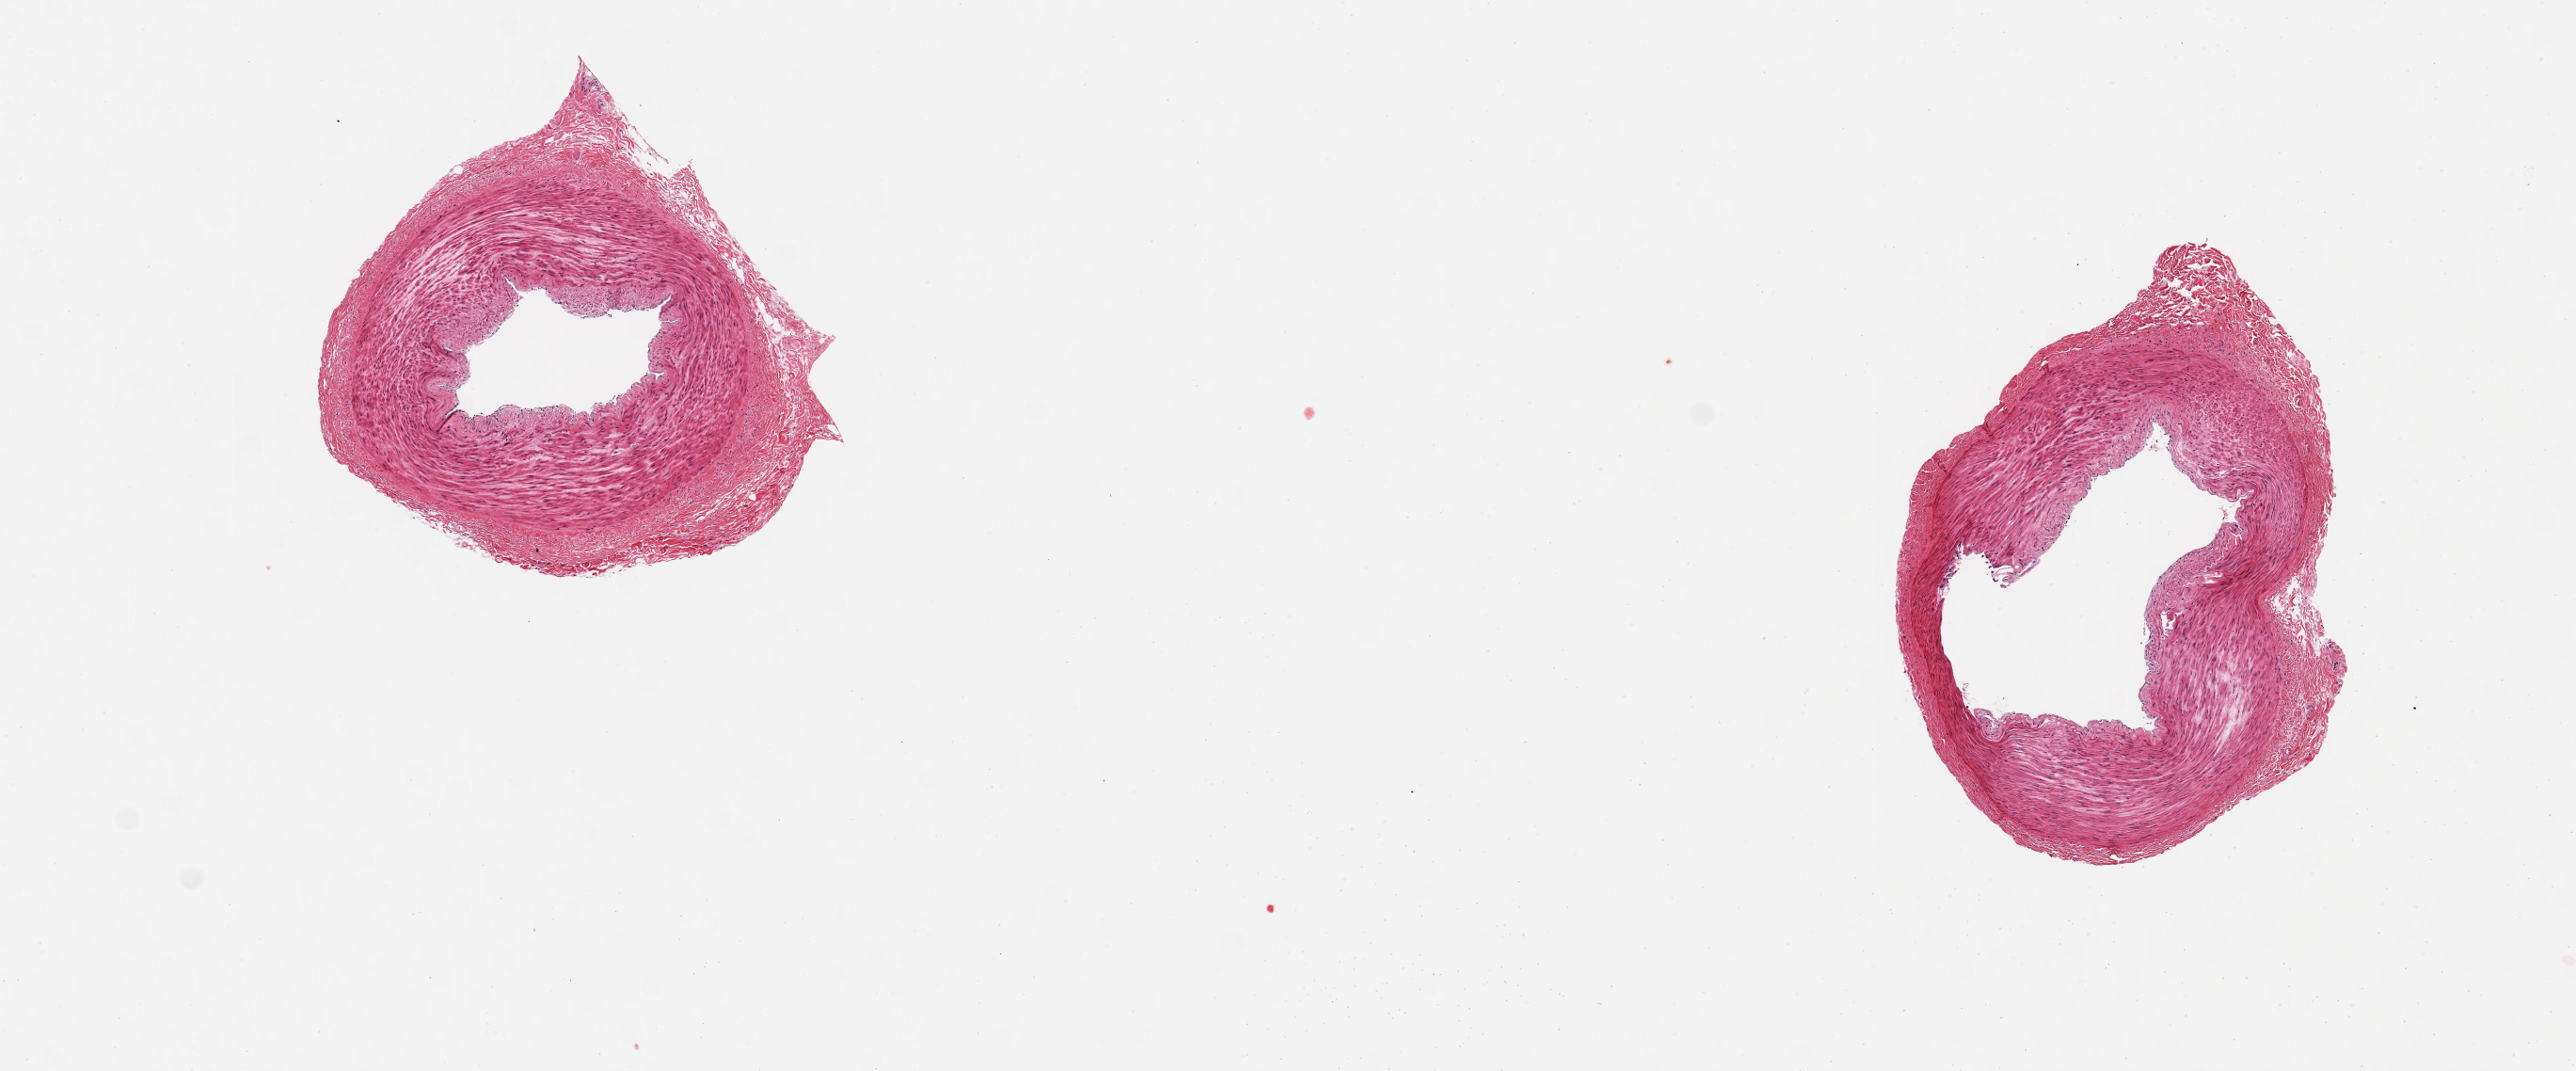
Hematoxylin and eosin (H&E) whole-slide image, brightfield — shown as a low-resolution overview of the whole scanned area (about 10.8 x 4.5 mm); PAXgene-fixed paraffin-embedded (PFPE) section; section of tibial artery (target tissue); donor tissue sample. Male donor.
Pathologist's review note for this sample: 2 pieces ~2mm d. Good clean specimens.